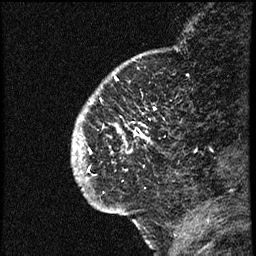
Breast MRI (dynamic contrast-enhanced), one sagittal slice; slice 13 of 66 in the series (ordered by position); dynamic contrast-enhanced study with each time point stored as its own series, time point 2 of 3 at this slice position (early post-contrast, ordered by acquisition time); 1.5 T; TE 4.2 ms, TR 17.6 ms; 2 mm slice thickness; 256 × 256 image matrix. Female patient. From the clinical record (not read from this slice): setting: breast cancer imaged before/during neoadjuvant chemotherapy; receptor status: HER2-positive.
Structures marked on this image (semi-automatic segmentation, software-assisted and operator-edited):
- analysis volume of interest (the breast-tissue region the enhancement analysis was run in; not a lesion): bounding box [x1, y1, x2, y2] px = [74, 69, 177, 209]
- tumour enhancement mask (voxels above the 100 % enhancement threshold inside the analysis volume of interest): [75, 129, 140, 180]